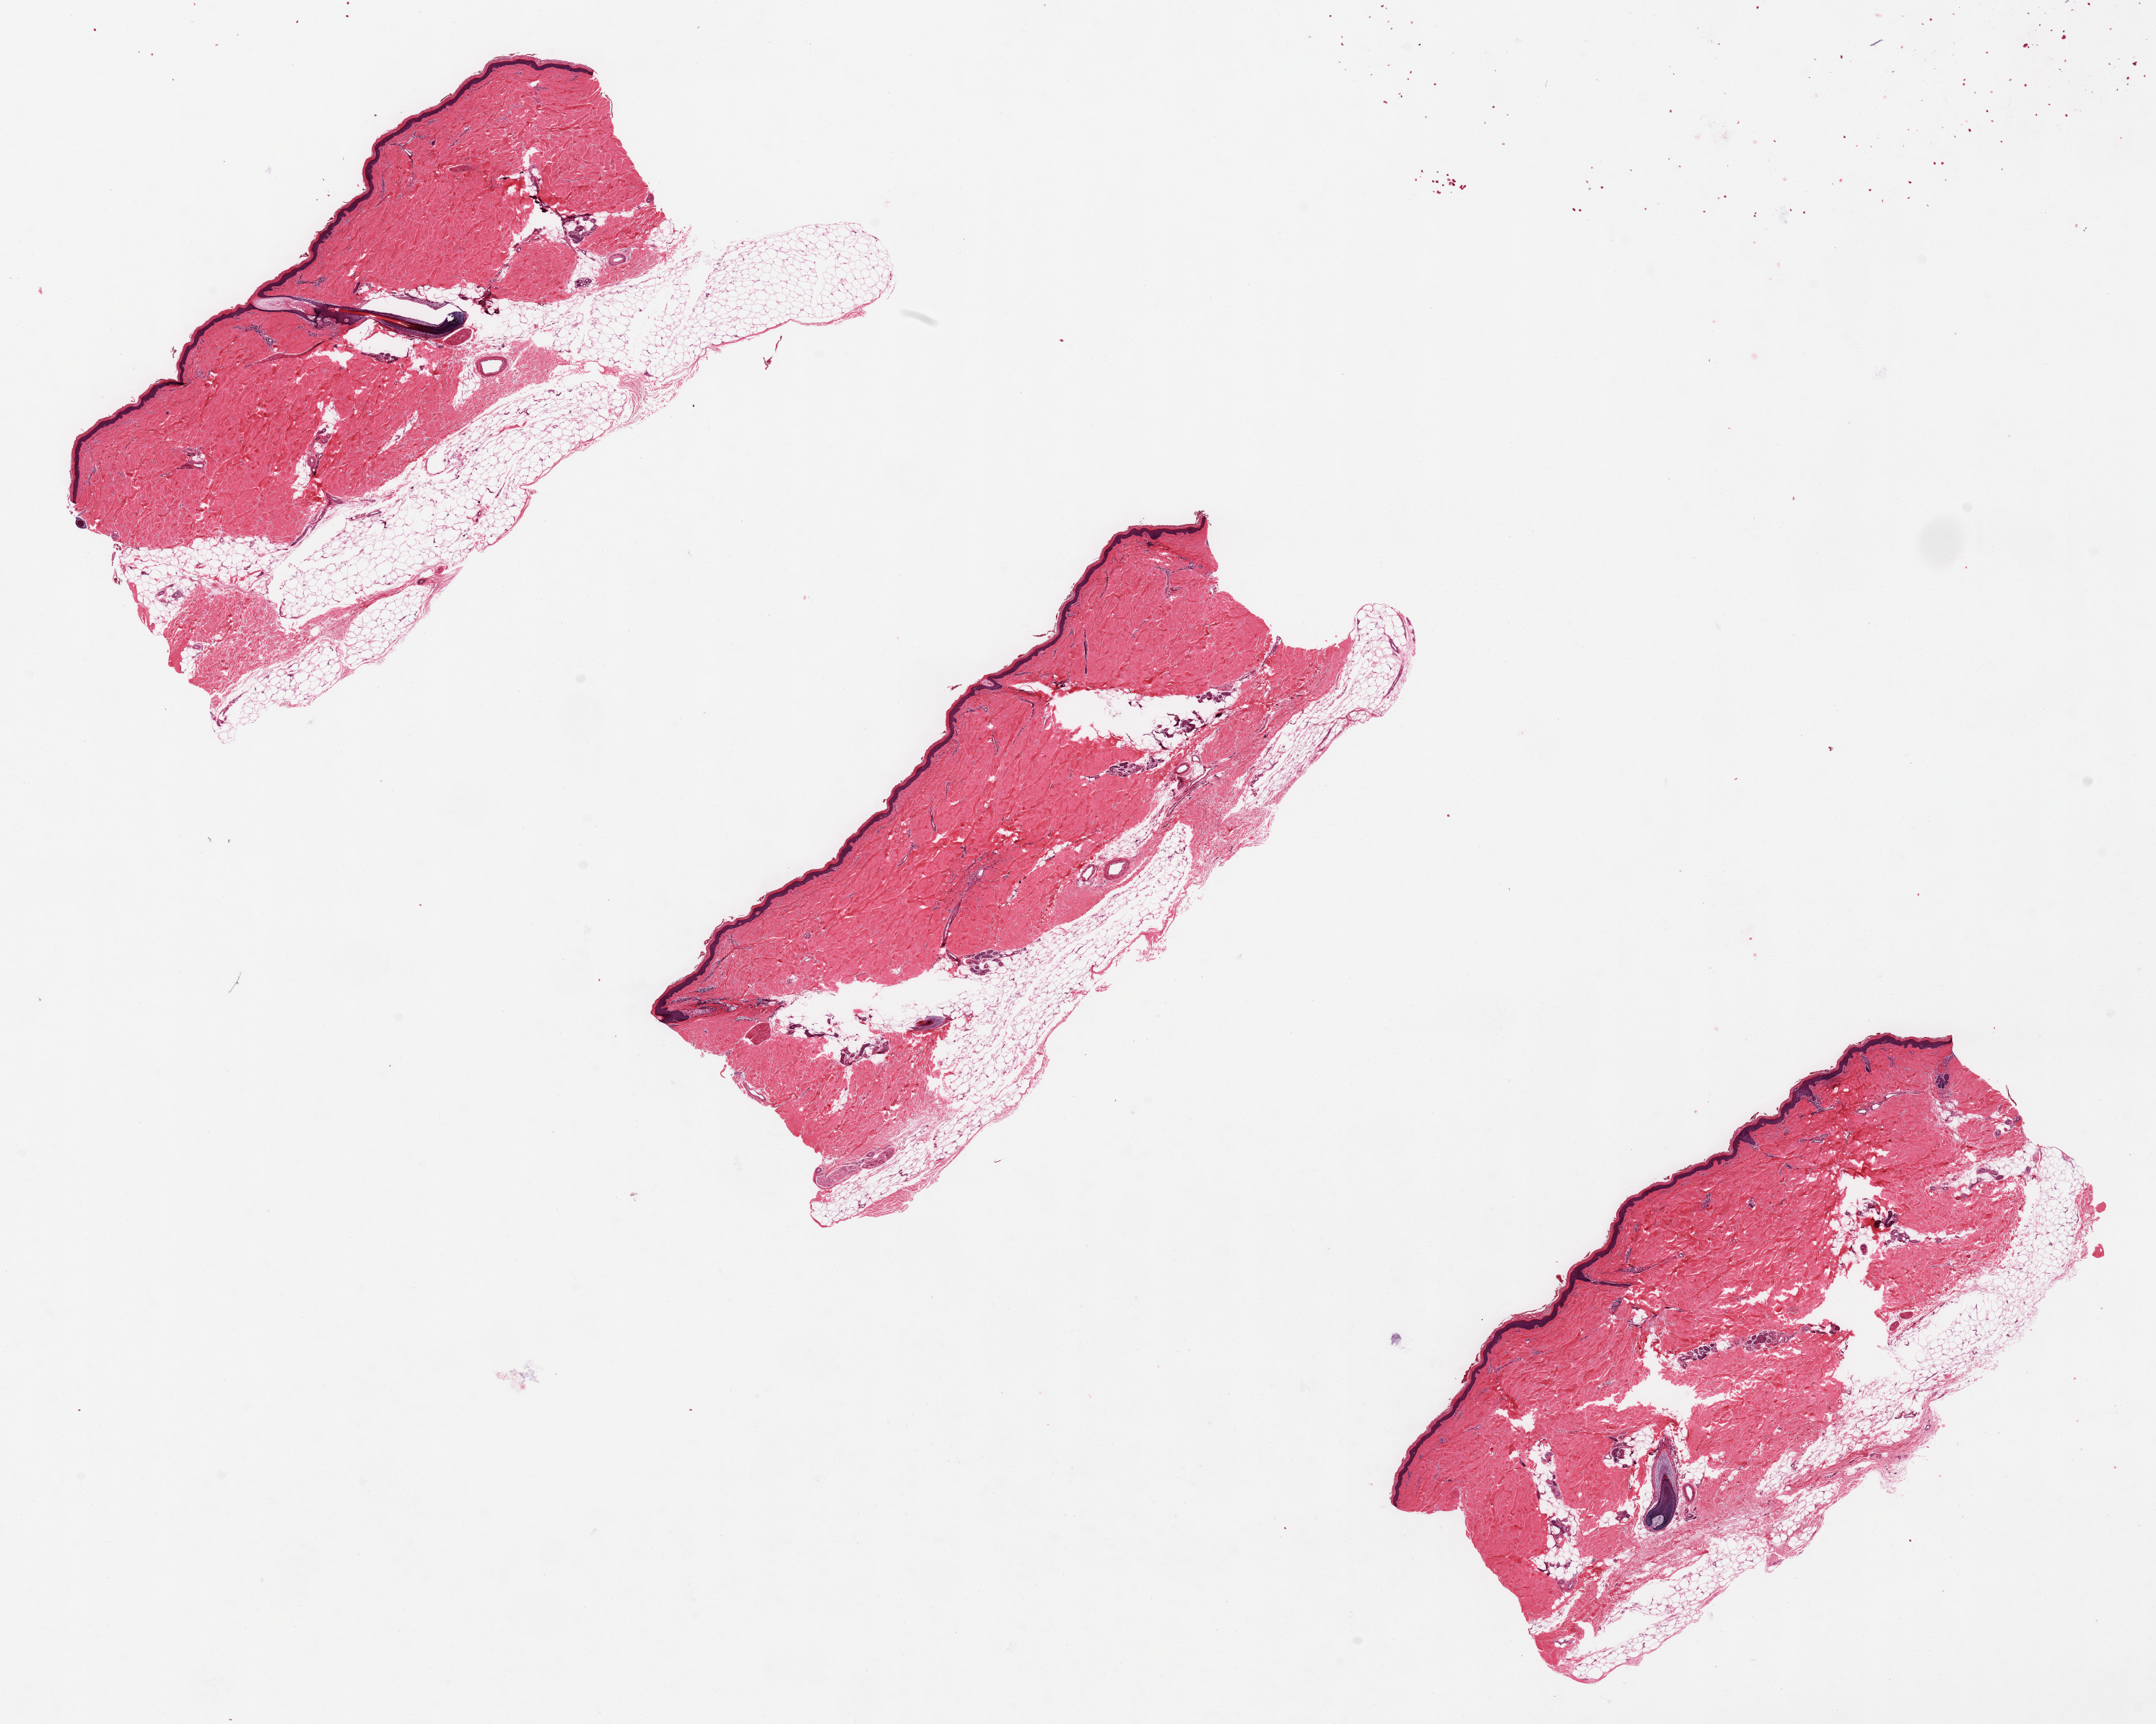
Hematoxylin and eosin (H&E) whole-slide image — low-resolution overview of the scanned area, about 23.6 x 18.9 mm. PAXgene-fixed, paraffin-embedded tissue. Sampled site (target tissue): skin of lower leg. Tissue donor sample. Male donor.
* pathologist's review note for this sample: Prominent defects along subcutaneous fat. 7.6x3.5 mm